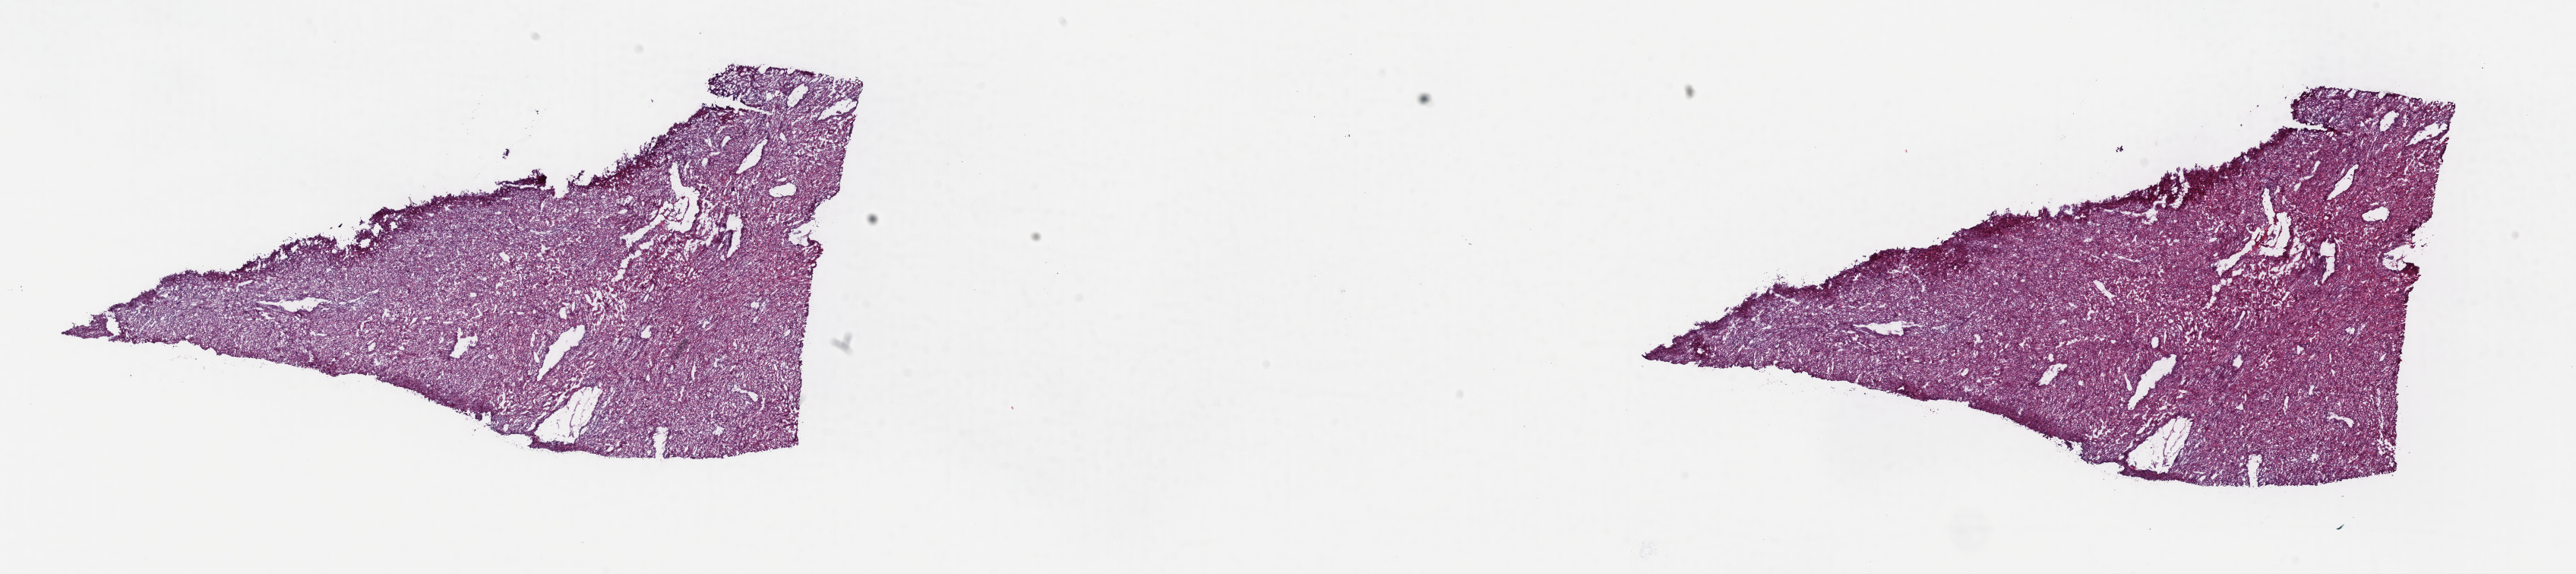
Whole-slide histology image, H&E, a low-resolution overview of the entire scanned area, about 26.8 x 6.0 mm (from a 40x scan). Frozen section. Retroperitoneum and peritoneum, primary tumour sample. Female patient; age at initial diagnosis 78 years. Composition of this section per pathologist review: tumour cells 90%, tumour nuclei 90%, normal cells 0%, stromal cells 10%, necrosis 0%. Infiltration values recorded for this section: lymphocyte infiltration 0%, monocyte infiltration 0%, neutrophil infiltration 0%.
Diagnosis: Dedifferentiated liposarcoma (retroperitoneum).